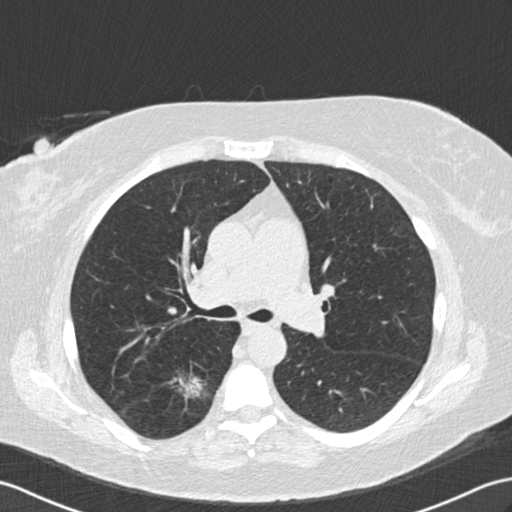
Low-dose screening chest CT, one axial slice; reconstruction kernel B30f; lung window (W 1500 / L -600 HU); 512 × 512 image matrix, field of view 352 × 352 mm.
Annotated regions visible in this slice (manually delineated by an expert):
- lesion 1 (tumor, lower lobe of right lung): bounding box [x1, y1, x2, y2] px = [177, 373, 206, 401]